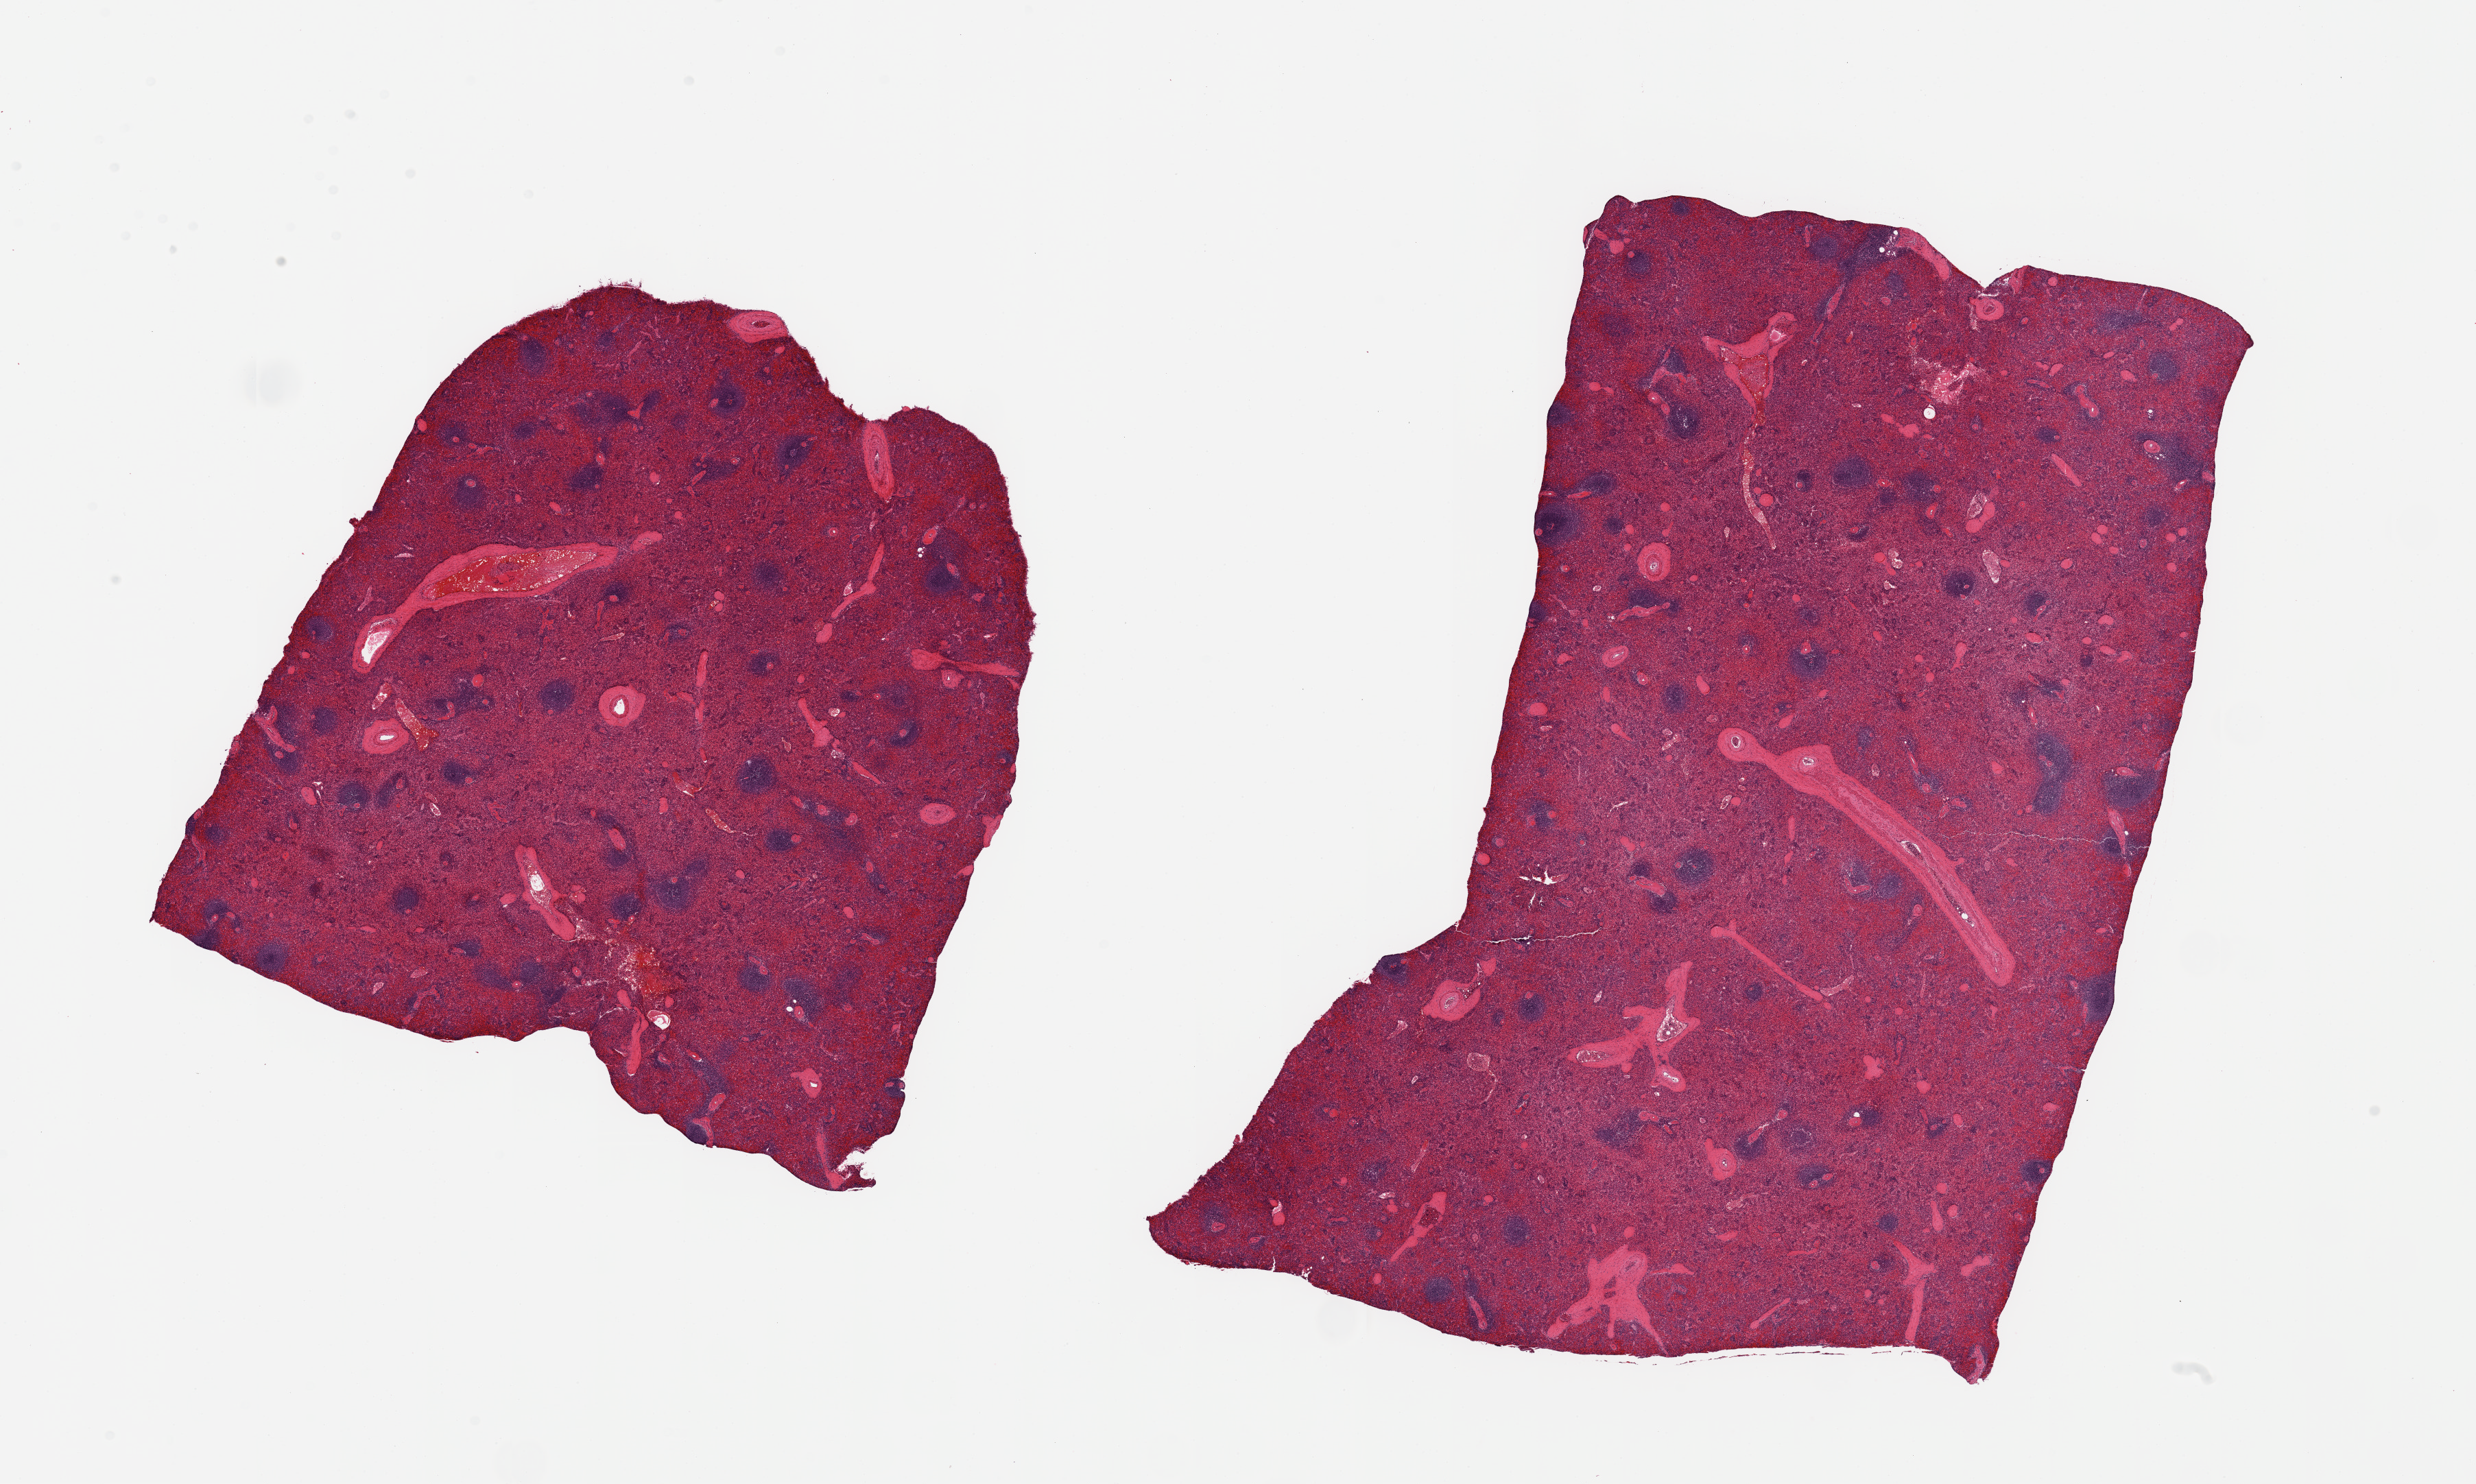
Hematoxylin and eosin (H&E) whole-slide image — a low-resolution overview of the entire scanned area, about 28.5 x 17.1 mm, PAXgene-fixed paraffin-embedded (PFPE) section, target tissue: spleen, tissue donor sample.
• review note (as recorded): 2 pieces; moderate congestion